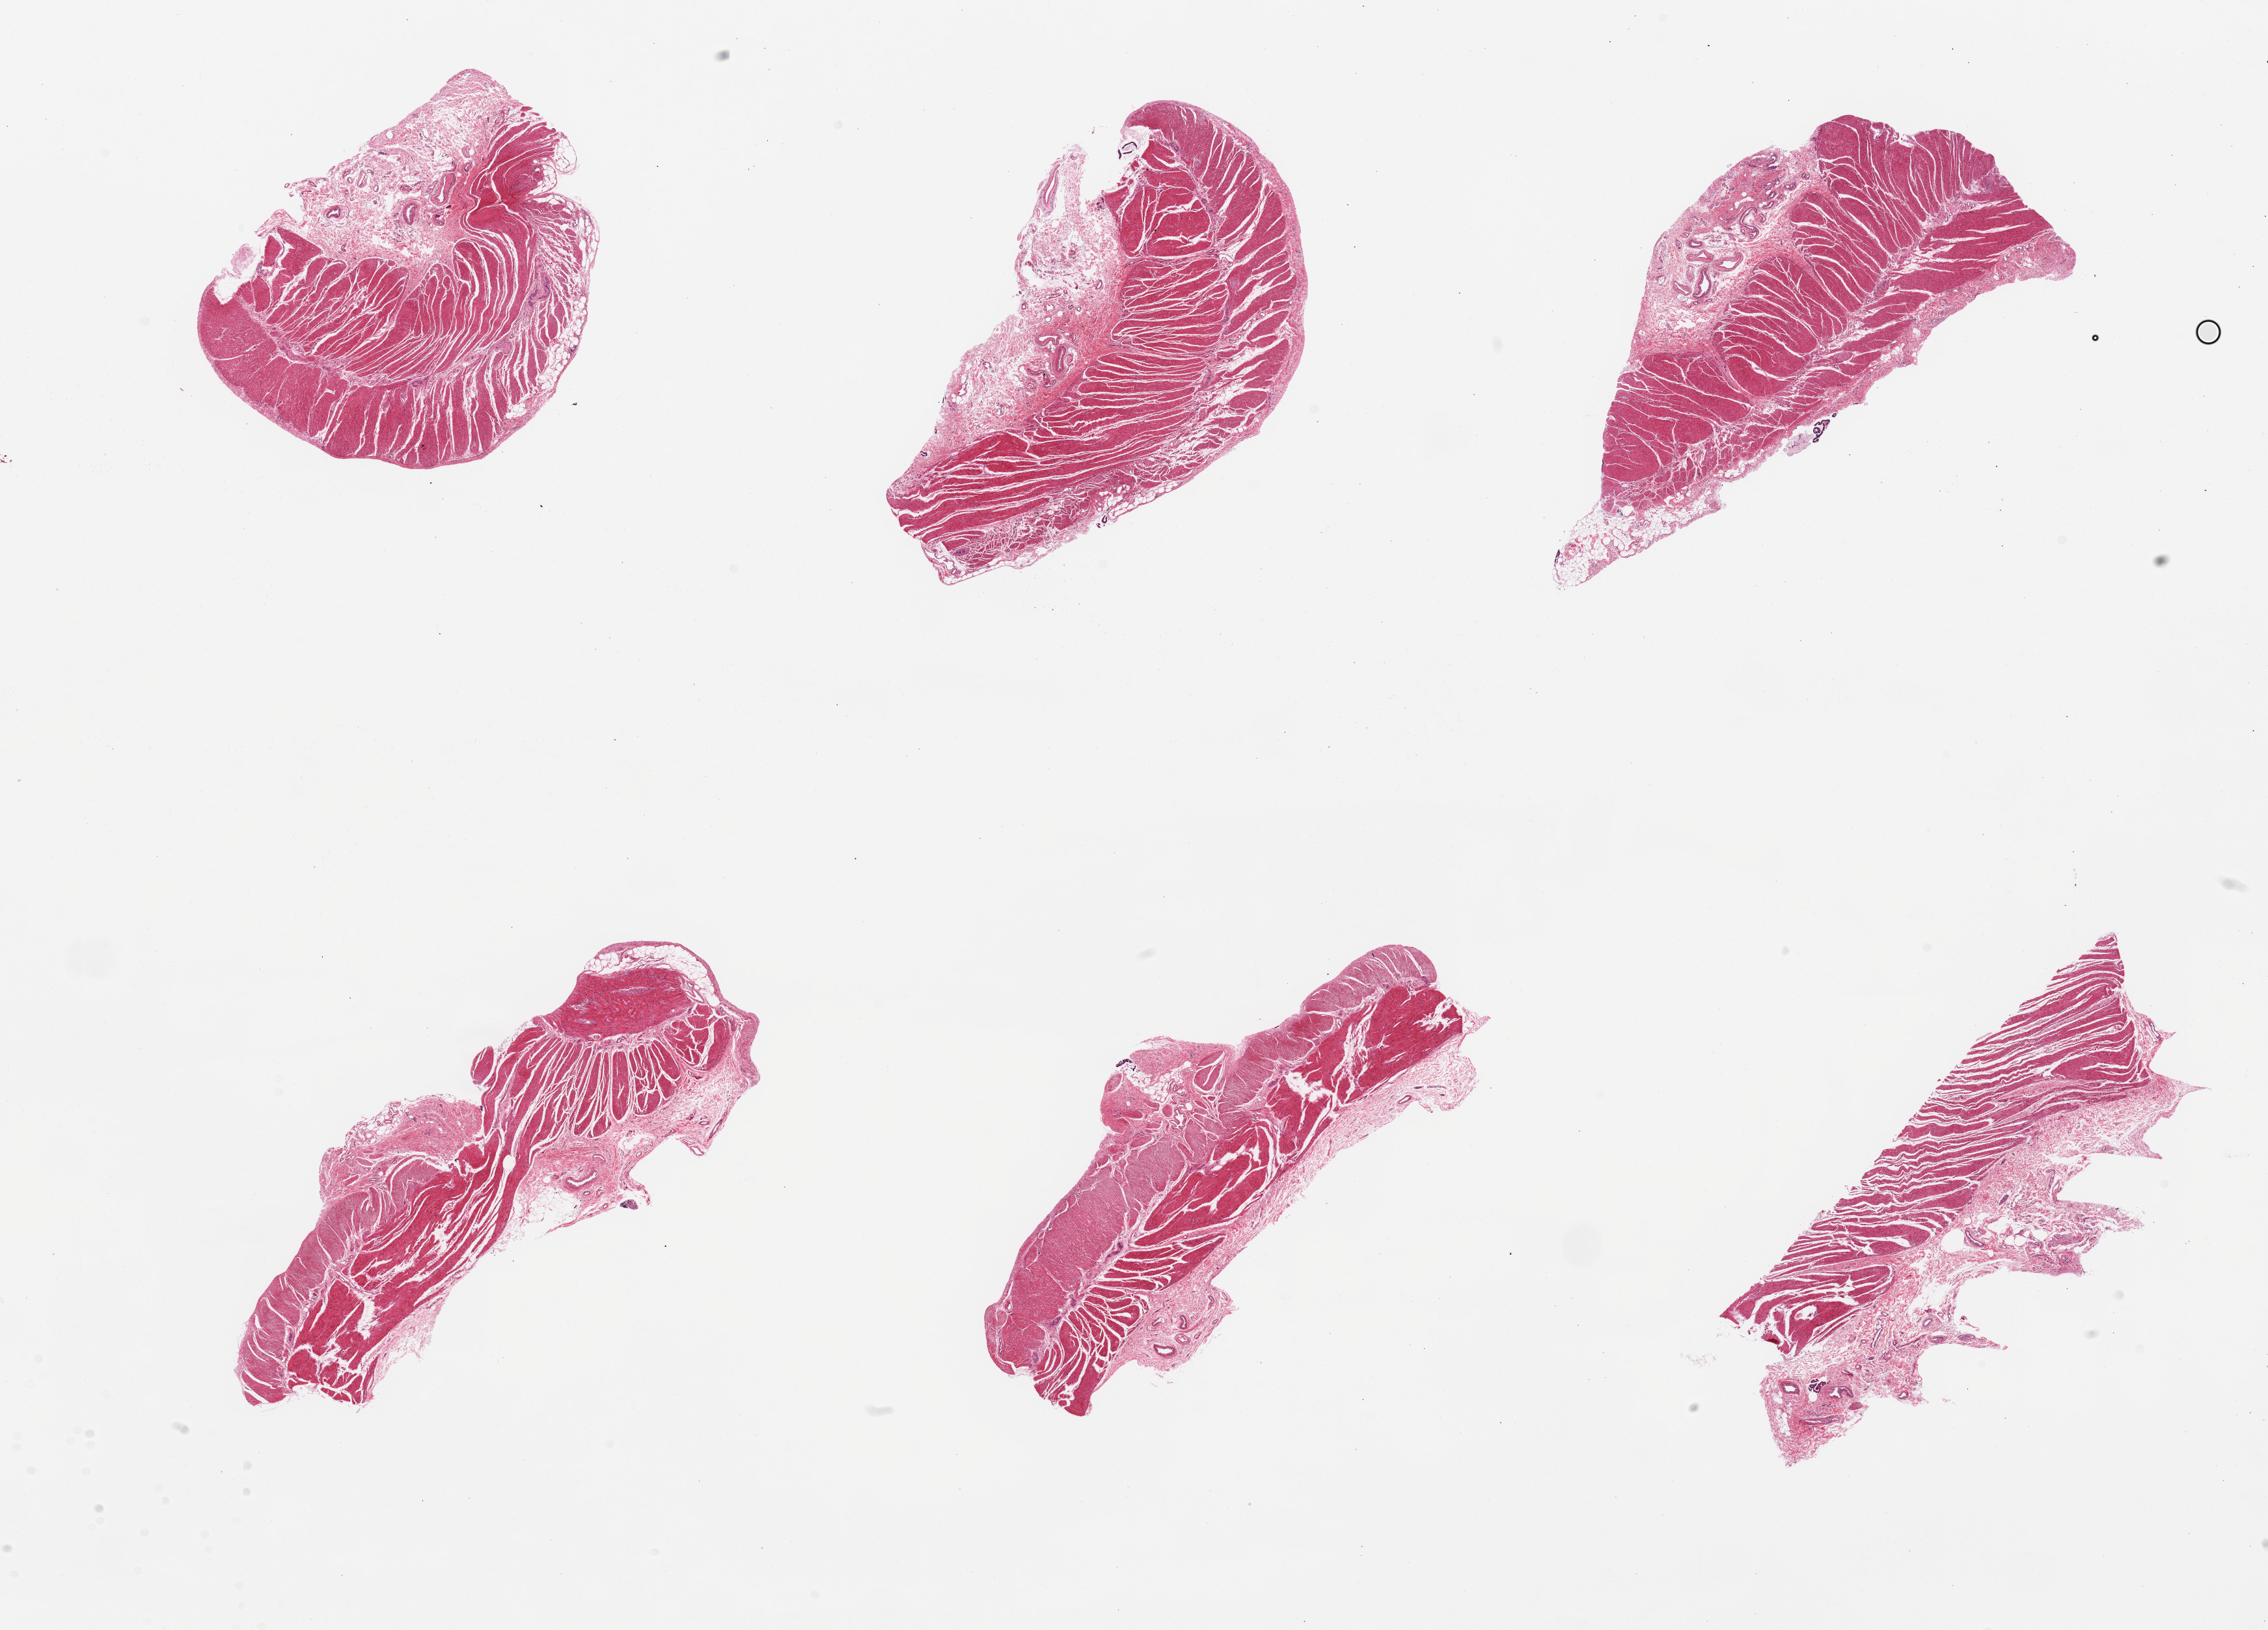
H&E whole-slide image, low-resolution overview of the scanned area, about 27.6 x 19.8 mm (acquisition: 20x scan), PAXgene-fixed, paraffin-embedded tissue, target tissue: sigmoid colon, tissue donor sample. Donor sex: female.
Reviewer comment on this tissue sample: 6 pieces, all muscularis/adherent fat/serosa.